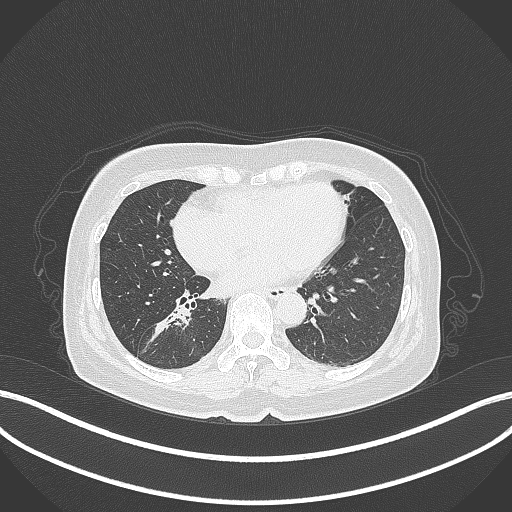
Chest CT, one axial slice; slice 157 of 429 in the series (ordered by position); 120 kVp; lung window (W 1500 / L -600 HU); 512 × 512 image matrix, field of view 400 × 400 mm. Patient: female, 67 years. Case-level facts recorded for this patient, not image findings: clinical TNM (as recorded): T1c N1 M0.
Outlined on this slice (rectangle marked by the reading radiologist):
- lung tumour (recorded histology: adenocarcinoma): bounding box [x1, y1, x2, y2] px = [144, 301, 194, 348]